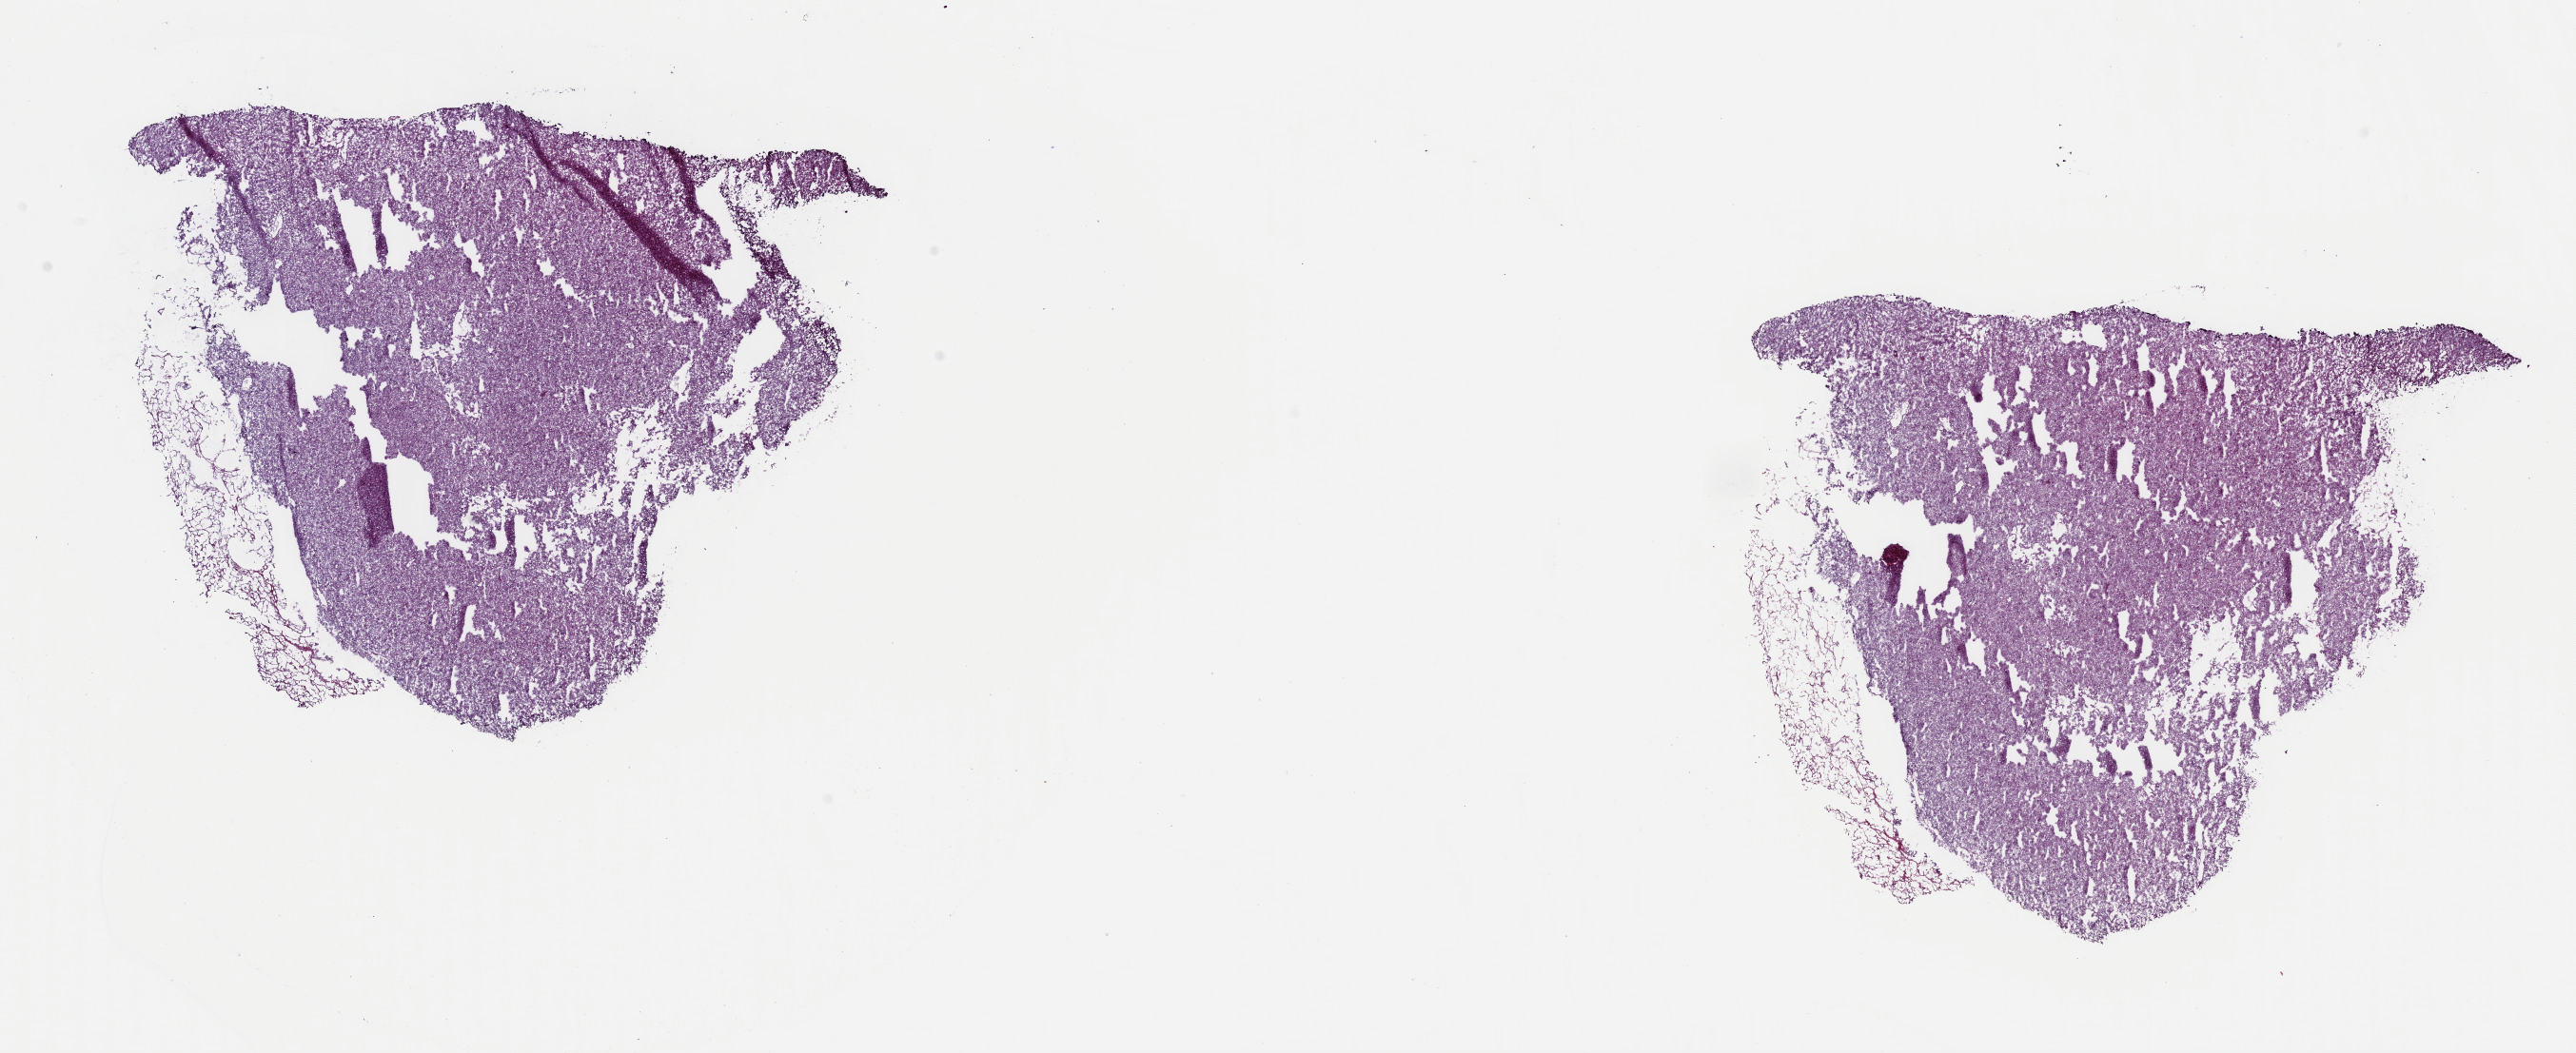
Whole-slide histology image, H&E-stained — shown as a low-resolution overview of the whole scanned area (about 21.4 x 8.7 mm, from a 40x scan); frozen section from the top of the tissue portion; sample: primary tumour, adrenal cortex. Patient: female, age at initial diagnosis 65 years. Pathologist review of this section (percent, as recorded): tumour cells 90%, tumour nuclei 90%, normal cells 0%, stromal cells 10%, necrosis 0%. Infiltration values recorded for this section: lymphocyte infiltration 0%, monocyte infiltration 0%, neutrophil infiltration 0%.
Pathologic diagnosis: Adrenal cortical carcinoma (cortex of adrenal gland).